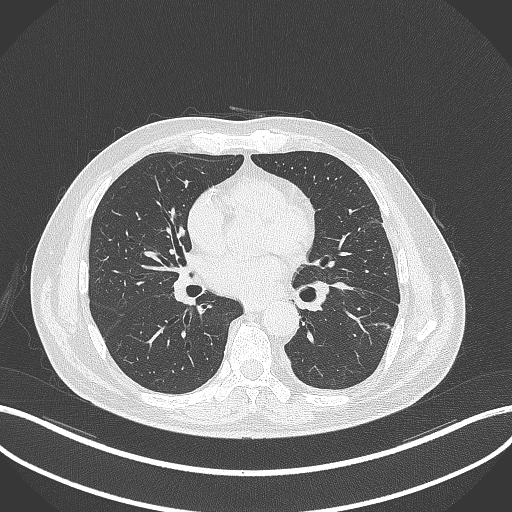
Chest CT, one axial slice; reconstruction kernel B70f; lung window (W 1500 / L -600 HU); 1 mm slice thickness; 512 × 512 image matrix. Patient: male, 68 years. Case-level facts recorded for this patient, not image findings: clinical TNM (as recorded): T2b N0 M0.
Annotated regions visible in this slice (rectangle marked by the reading radiologist):
- lung tumour (recorded histology: squamous cell carcinoma): bounding box [x1, y1, x2, y2] px = [327, 277, 361, 297]